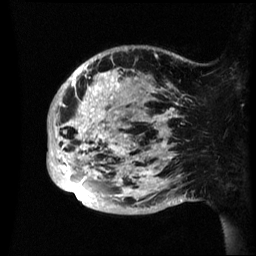
Breast MRI (dynamic contrast-enhanced), one sagittal slice. Position 15 of 60 along the scan axis. Dynamic contrast-enhanced series, image 2 of 3 at this slice position (ordered by acquisition). 1.5 T. TE 4.2 ms, TR 8.4 ms. 2.4 mm slice thickness. 256 × 256 image matrix, field of view 230 × 230 mm. Female patient, age 48 years.
Annotated regions visible in this slice (semi-automatic segmentation, software-assisted and operator-edited):
- analysis volume of interest (the breast-tissue region the enhancement analysis was run in; not a lesion): bounding box [x1, y1, x2, y2] px = [47, 46, 195, 215]
- tumour enhancement mask (voxels above the 70 % enhancement threshold inside the analysis volume of interest): [47, 67, 178, 199]